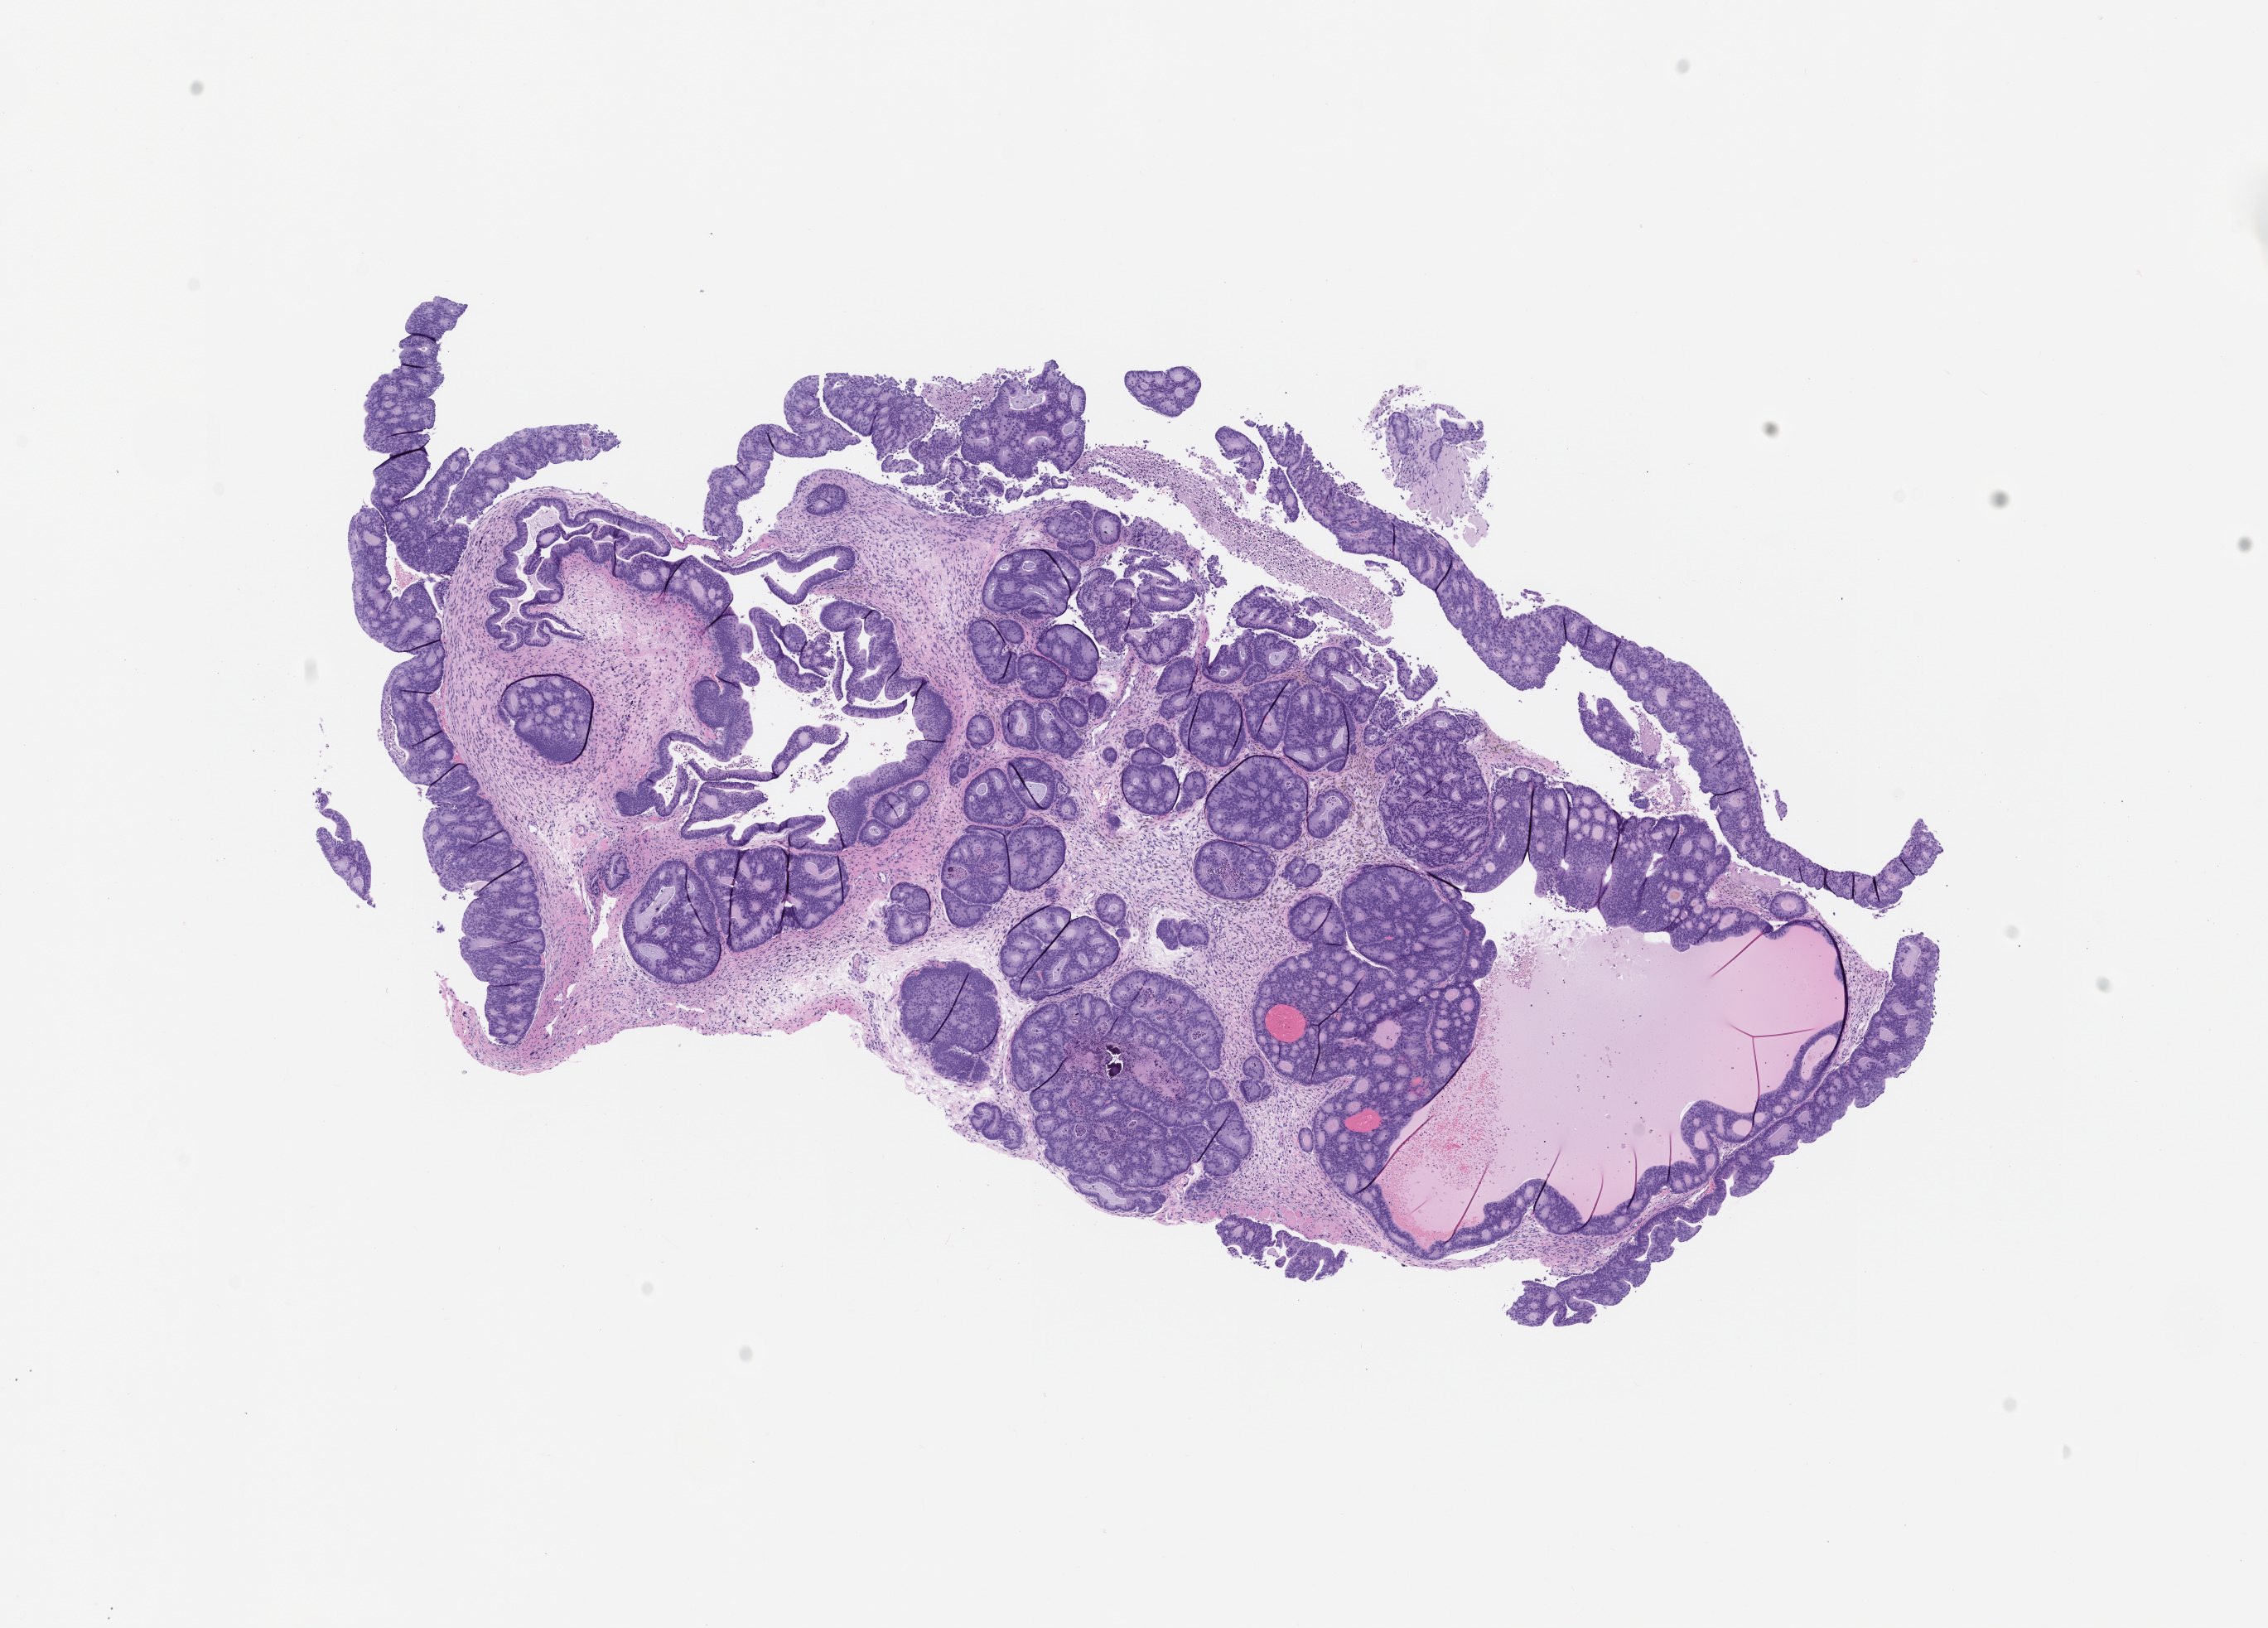
Hematoxylin and eosin (H&E) whole-slide image of a patient-derived xenograft (PDX) tumor grown in a mouse, passage 0 — whole scanned area (about 11.0 x 7.9 mm) shown as a low-resolution overview, formalin-fixed paraffin-embedded section, originating tumor site category: colon.
Originating patient diagnosis: Colon Adenocarcinoma.